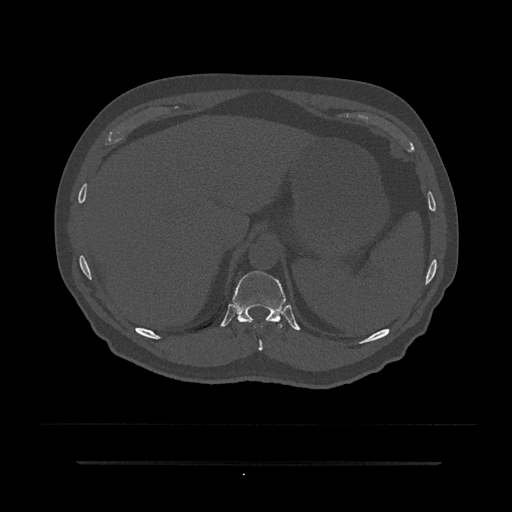
CT including the spine, one axial slice; position 289 of 797 along the scan axis; reconstruction kernel Br40s/3; 120 kVp; bone window (W 1800 / L 400 HU); 0.5 mm slice thickness; 512 × 512 image matrix, field of view 464 × 464 mm. Patient: male, 59 years. From the clinical record (not read from this slice): primary cancer: bile ducts; vertebrae with lytic lesions (as recorded): T10.
Structures marked on this image (semi-automatically segmented with operator editing):
- T10 vertebra: box from (x=238, y=320) to (x=274, y=351) px
- T11 vertebra: (x=232, y=271)–(x=286, y=328)